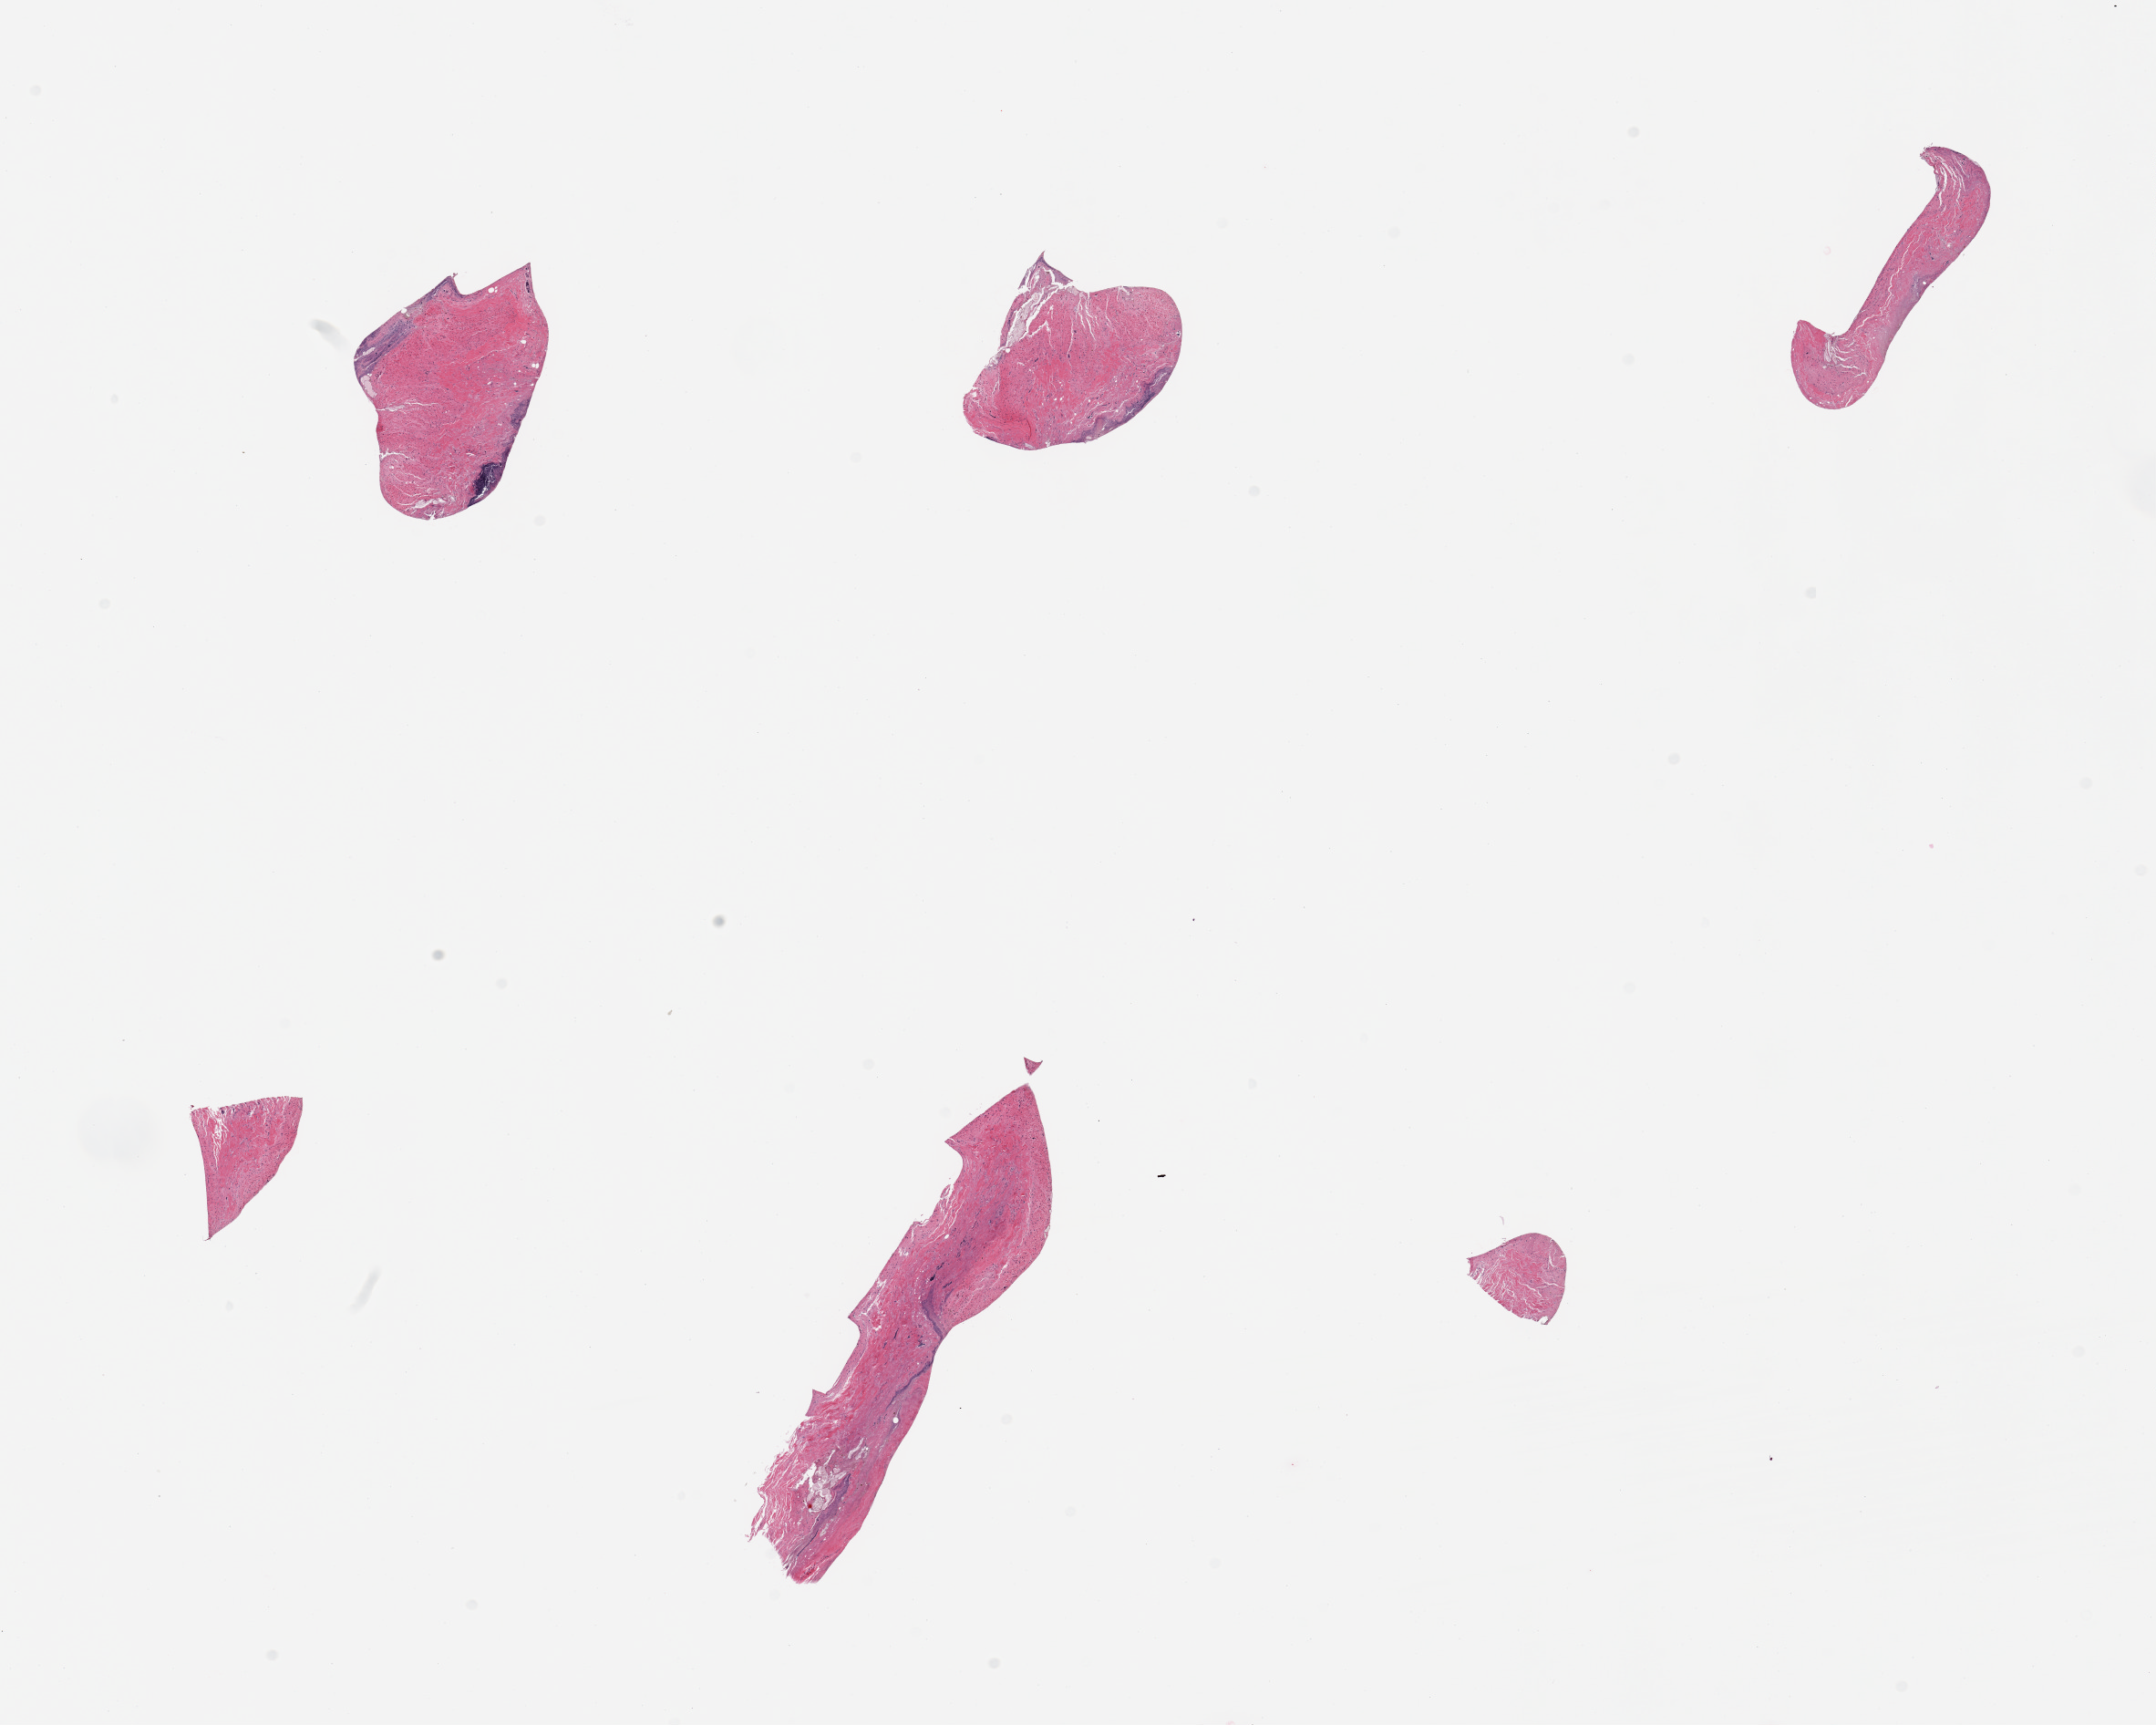
H&E whole-slide image, shown as a low-resolution overview of the whole scanned area (about 18.7 x 15.0 mm). PAXgene-fixed, paraffin-embedded tissue. Section of ileum (target tissue). Donor tissue sample. Female donor.
Review note (as recorded): 6 pieces; fragments of autolyzed mucosa (no lymphoid nodules) and muscularis.